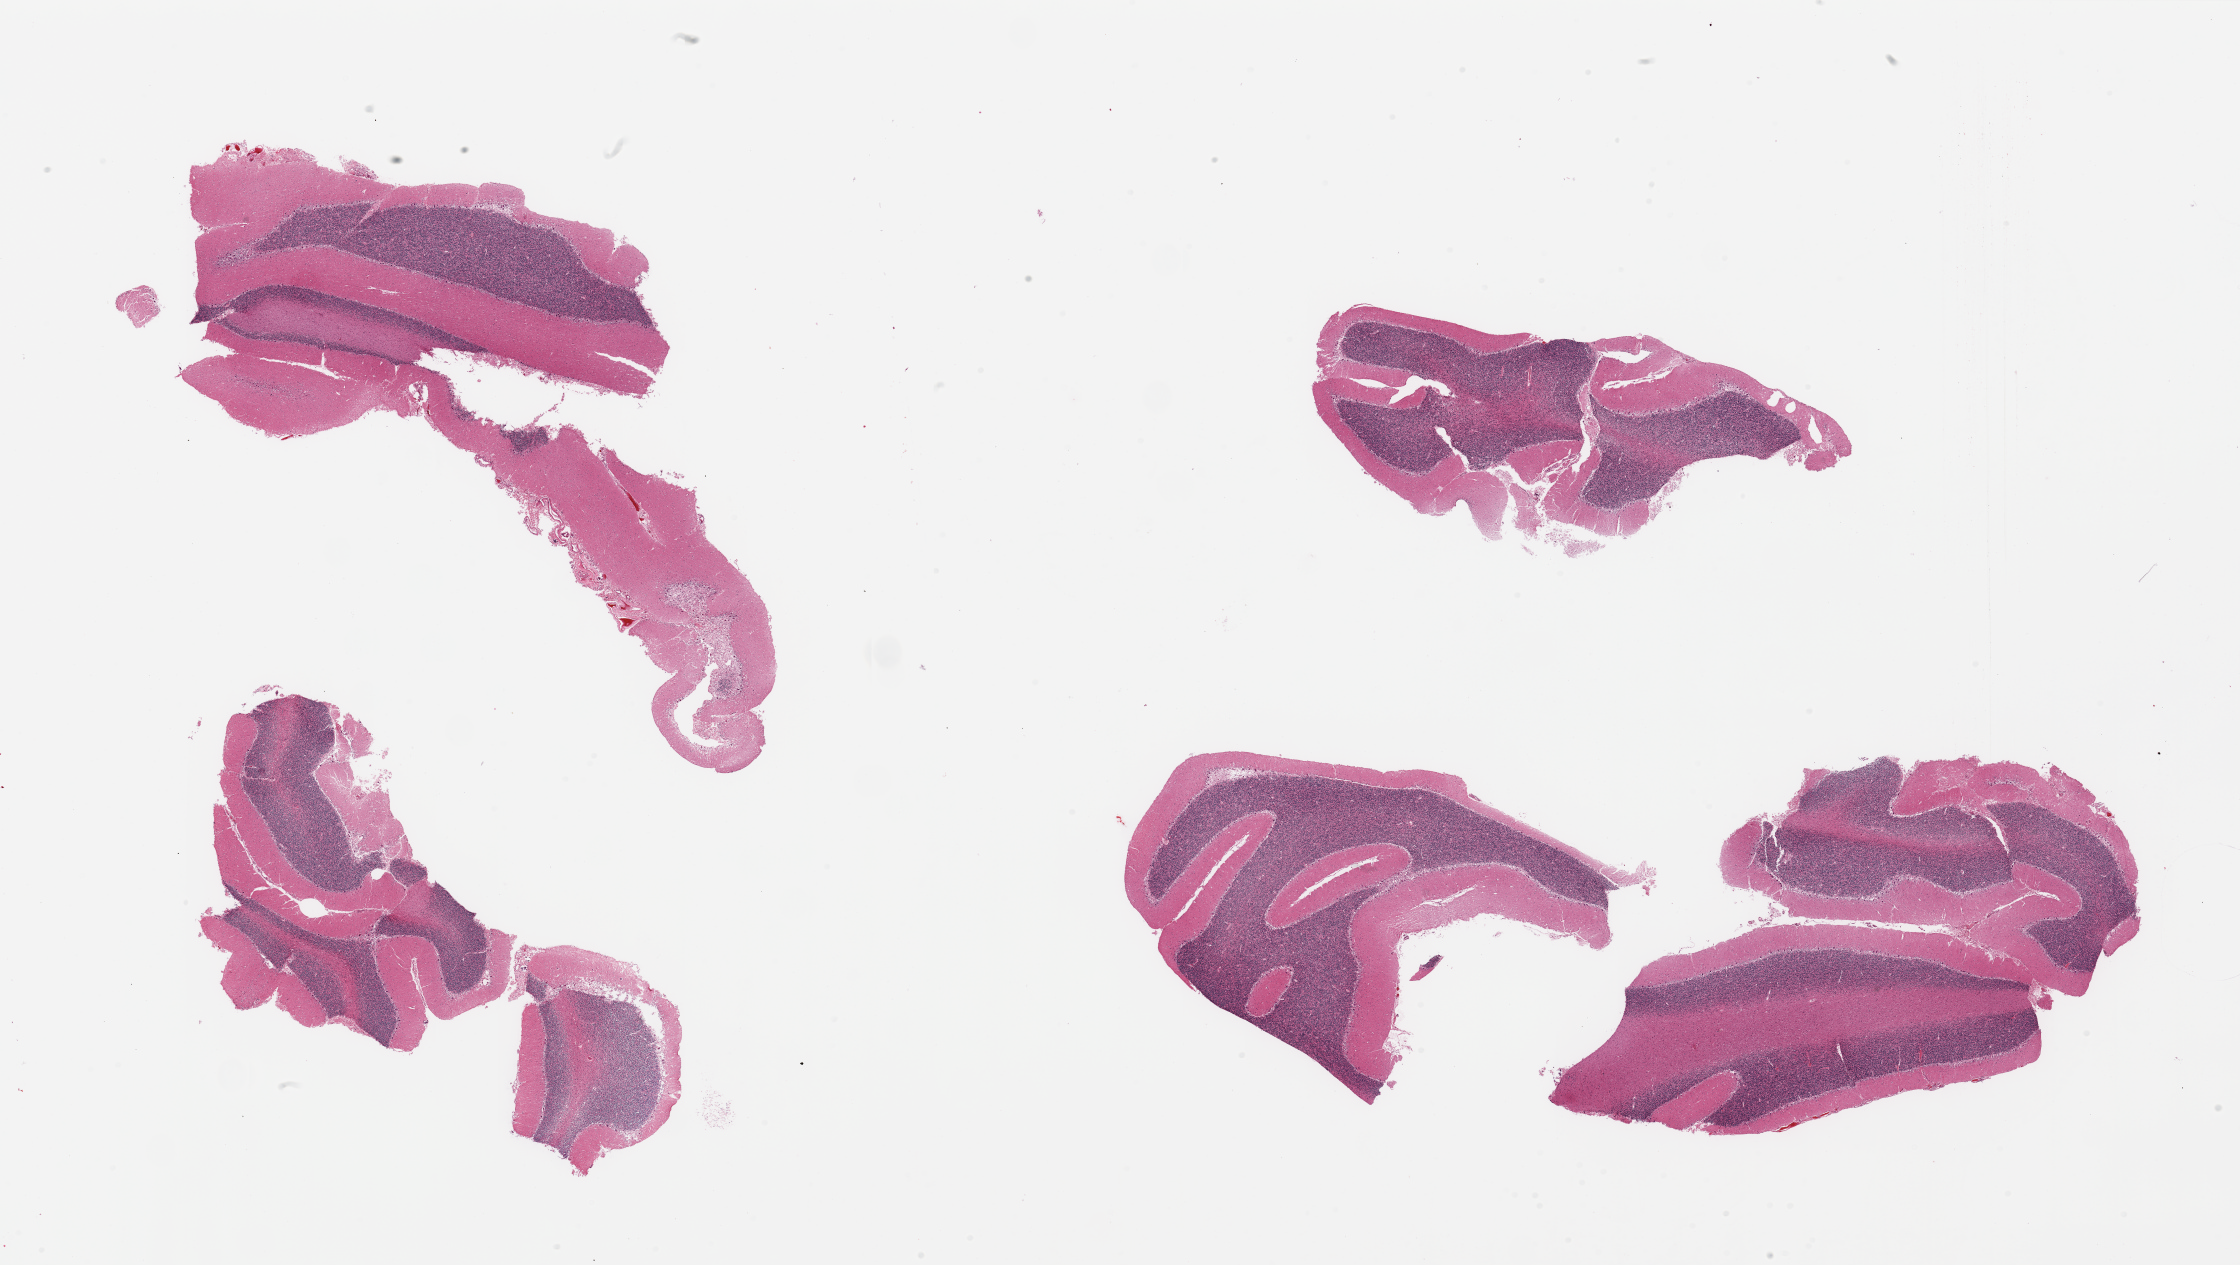
Digitized hematoxylin and eosin (H&E)-stained section, brightfield — whole scanned area (about 35.4 x 20.0 mm) shown as a low-resolution overview; PAXgene-fixed paraffin-embedded (PFPE) section; target tissue: cerebellum; donor tissue sample. Donor: female.
- pathologist's review note for this sample: 5 pieces; mild to moderate autolysis